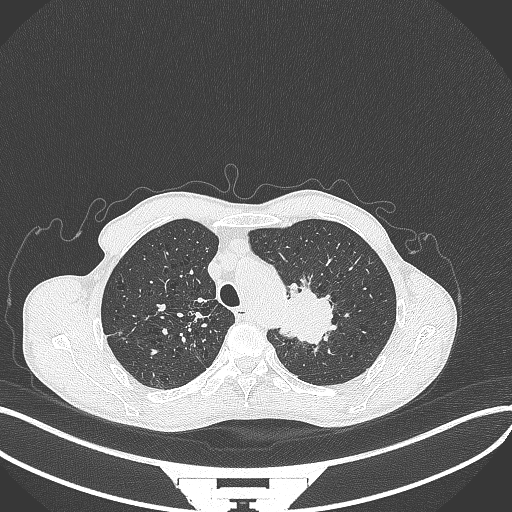
Chest CT, one axial slice. Position 329 of 386 along the scan axis. Lung window (W 1500 / L -600 HU). 1 mm slice thickness. 512 × 512 image matrix, field of view 400 × 400 mm. Patient: male, 65 years. From the clinical record (not read from this slice): clinical TNM (as recorded): T2b N0 M0; histopathological grade: G2.
Structures marked on this image (rectangle marked by the reading radiologist):
- lung tumour (recorded histology: adenocarcinoma): box from (x=278, y=278) to (x=340, y=347) px